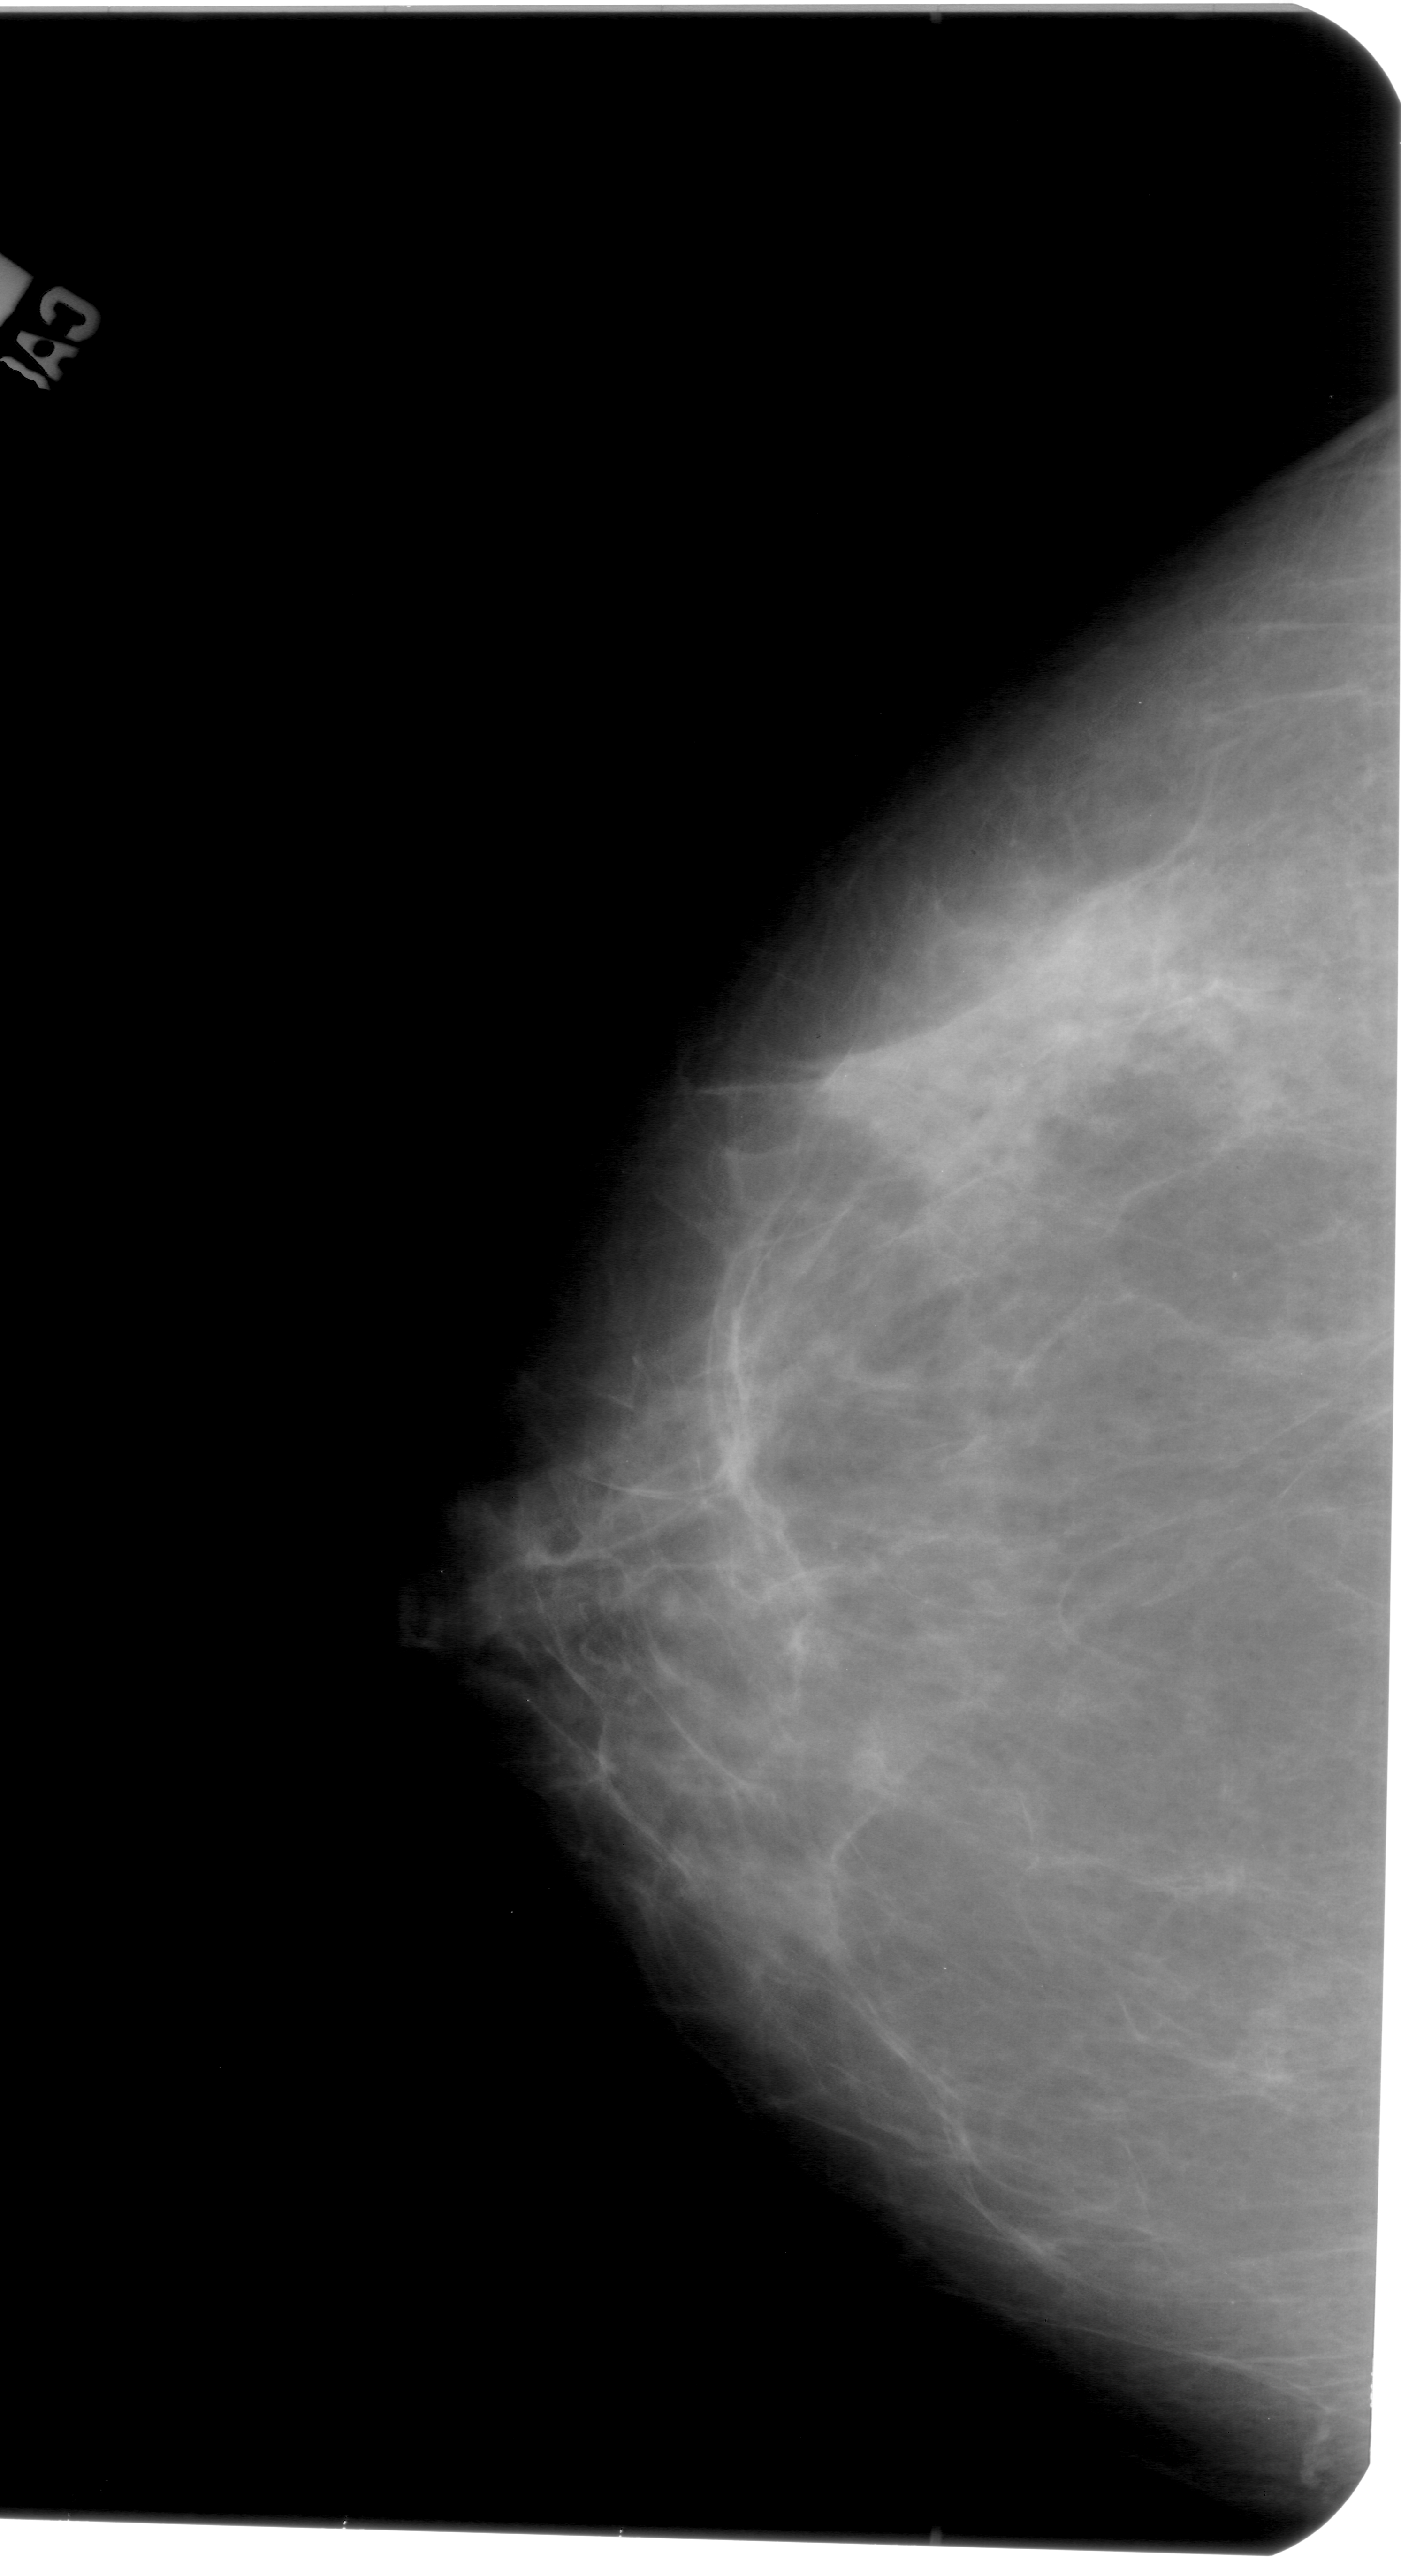
Scanned film-screen mammogram; left breast; craniocaudal (CC) view; breast composition: heterogeneously dense (BI-RADS density category 3 of 4); 1401 × 2576 image matrix.
Expert-marked regions of interest on this film, with their recorded descriptors:
- calcifications, morphology pleomorphic, distribution clustered; BI-RADS assessment category 4; pathology result (as recorded, not read from the image): benign: bounding box <1077,936,1277,1129> (left, top, right, bottom; pixels)